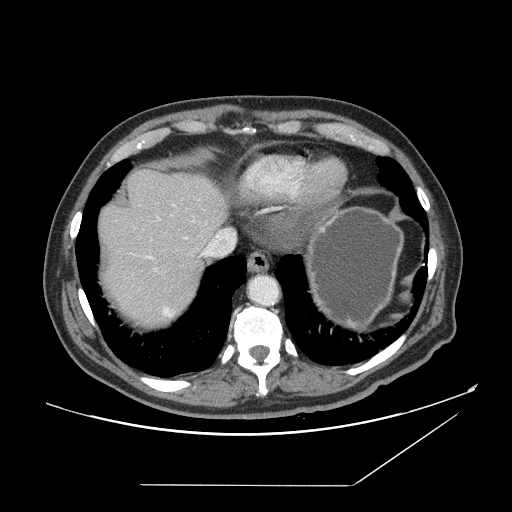
Contrast-enhanced abdominal CT, one axial slice; slice 134 of 166 in the series (ordered by position); soft-tissue window (W 400 / L 40 HU); 2.5 mm slice thickness; 512 × 512 image matrix. Male patient, age 80 years. Case-level facts recorded for this patient, not image findings: diagnosis: colorectal cancer liver metastases, imaged before liver resection; multiple liver metastases: no; largest metastasis: 2.2 cm; disease in both lobes: no.
Structures marked on this image (outlined manually by an expert reader):
- hepatic veins: bounding box [x1, y1, x2, y2] px = [146, 220, 235, 259]
- liver: [98, 169, 228, 328]
- planned liver remnant (the part of the liver to remain after resection): [98, 169, 228, 259]